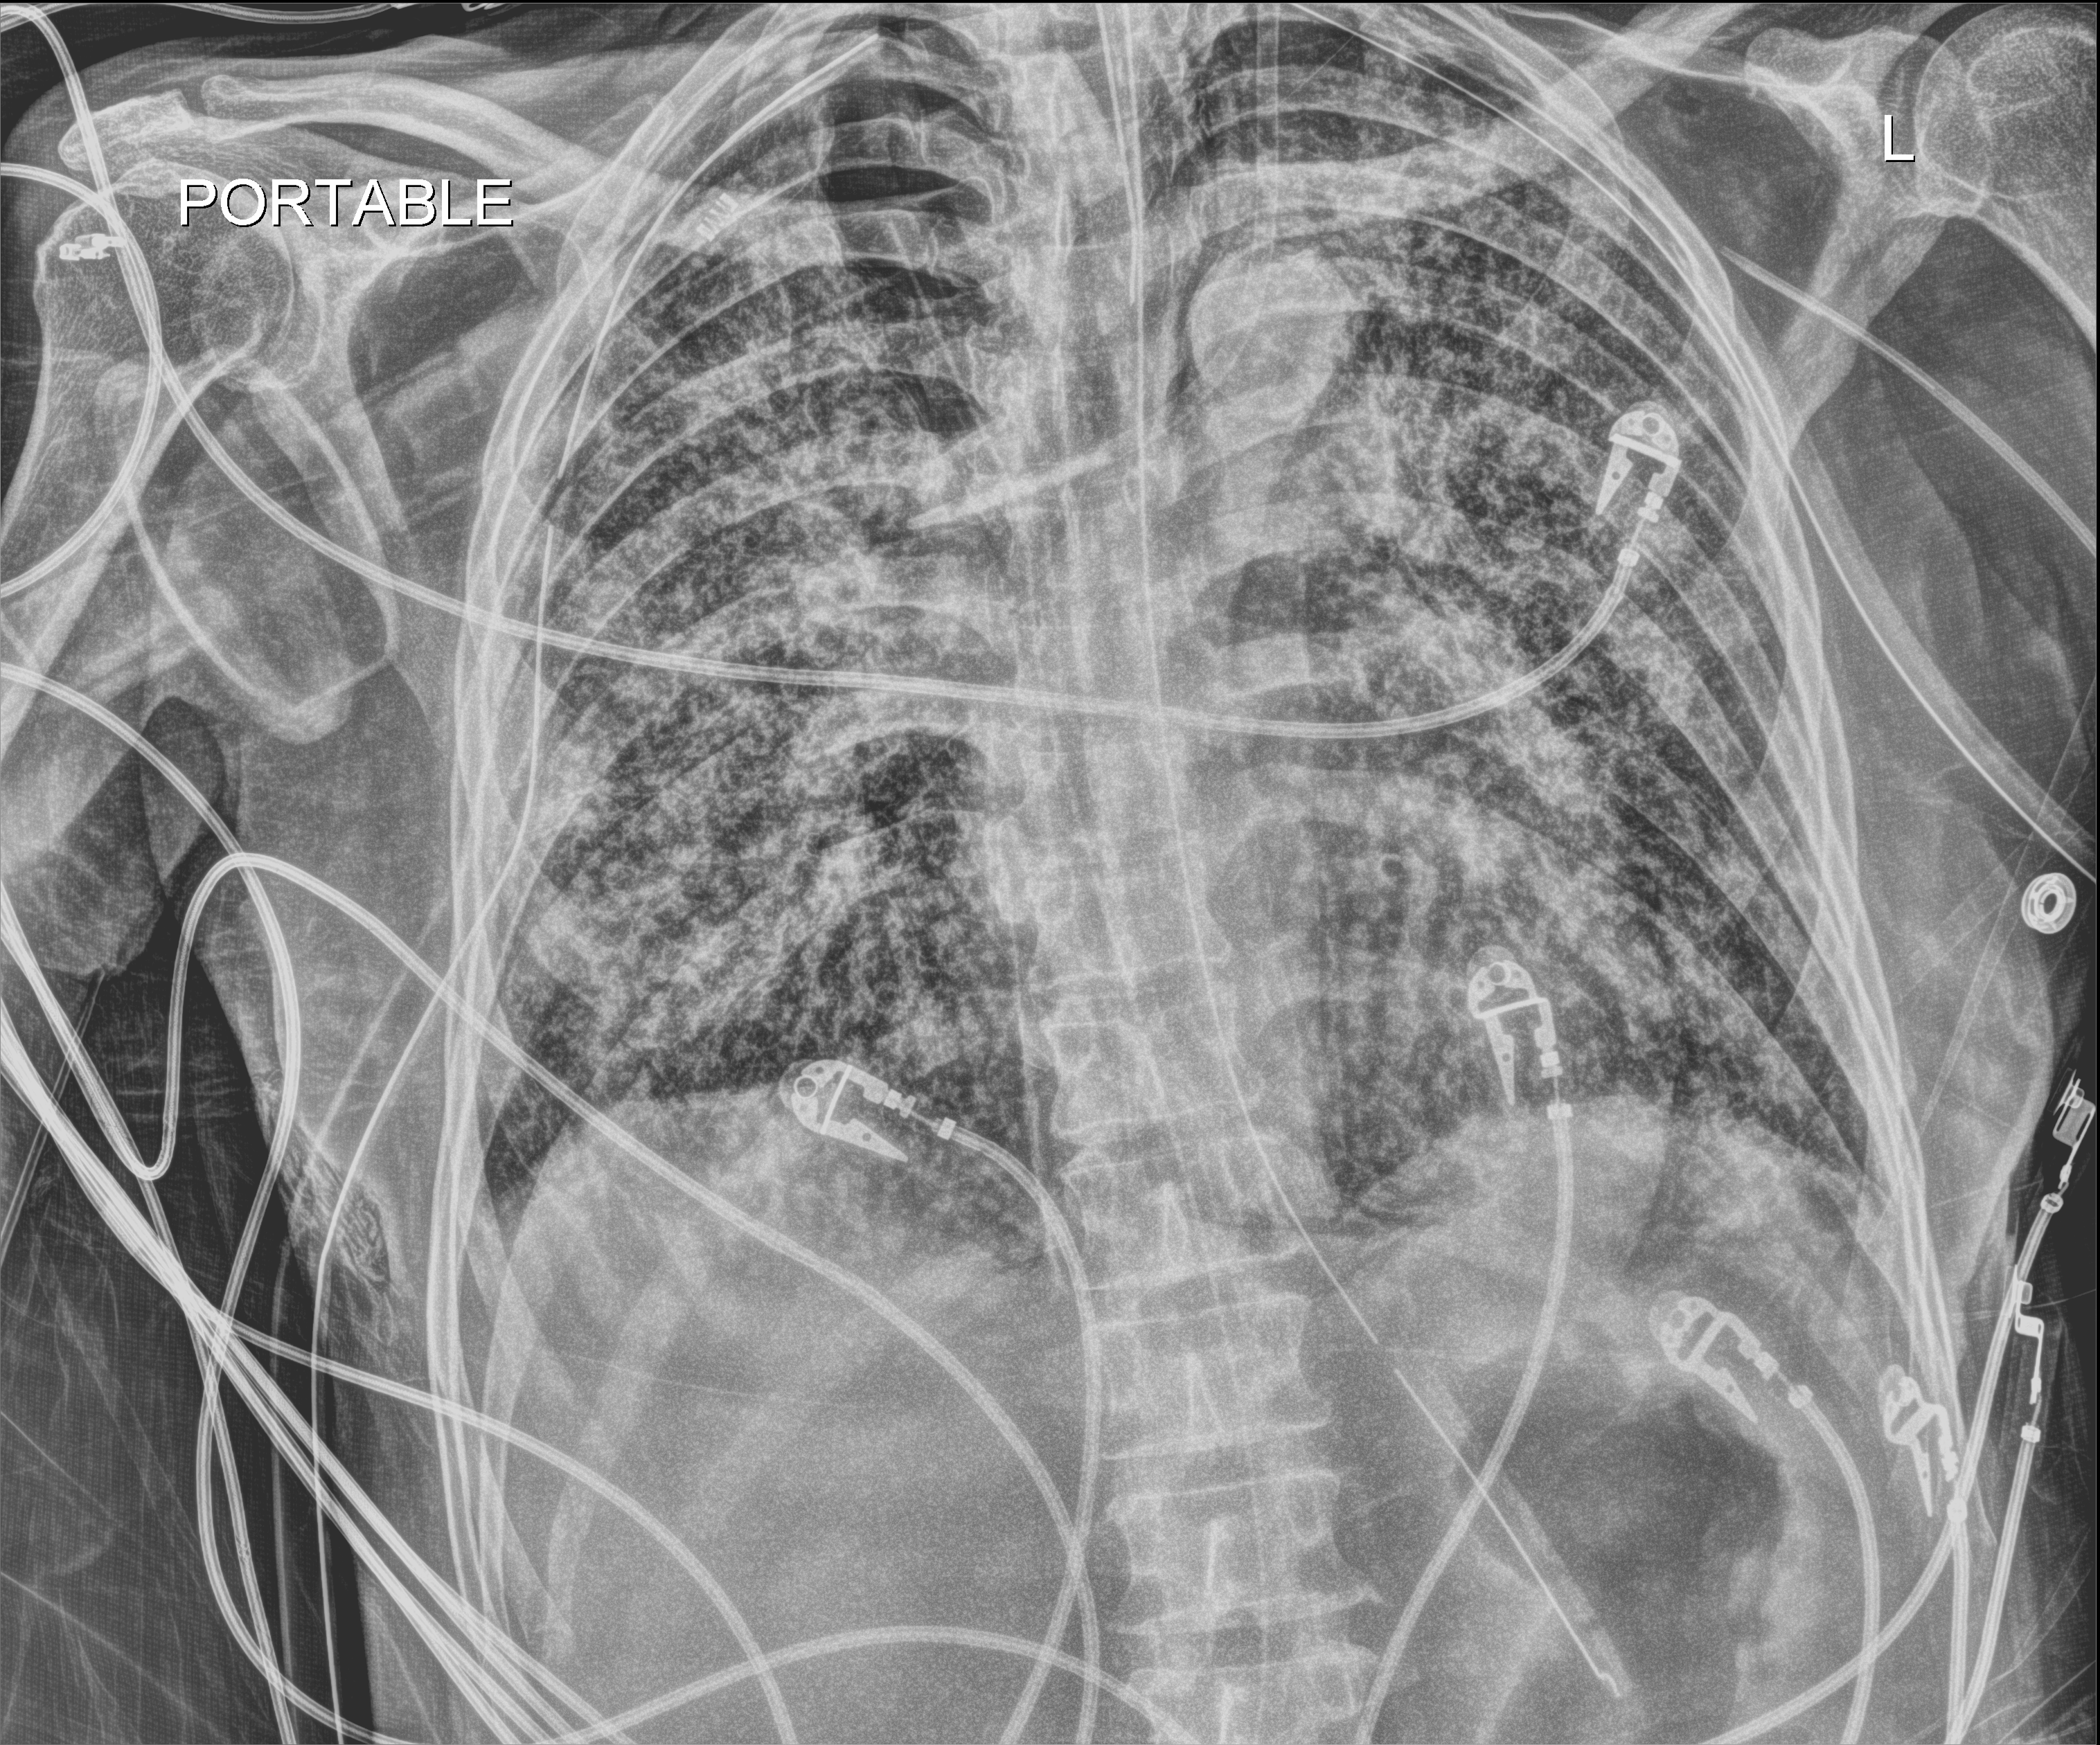
Portable chest radiograph, anteroposterior (AP) projection. Patient hospitalised with COVID-19; male, aged 60–74 years.
Admission-level facts for this patient (not findings on this image; timing relative to this image not recorded):
- length of hospital stay: 65 days
- other chronic lung disease (admission record): yes
- admitted to intensive care during this hospital stay: yes